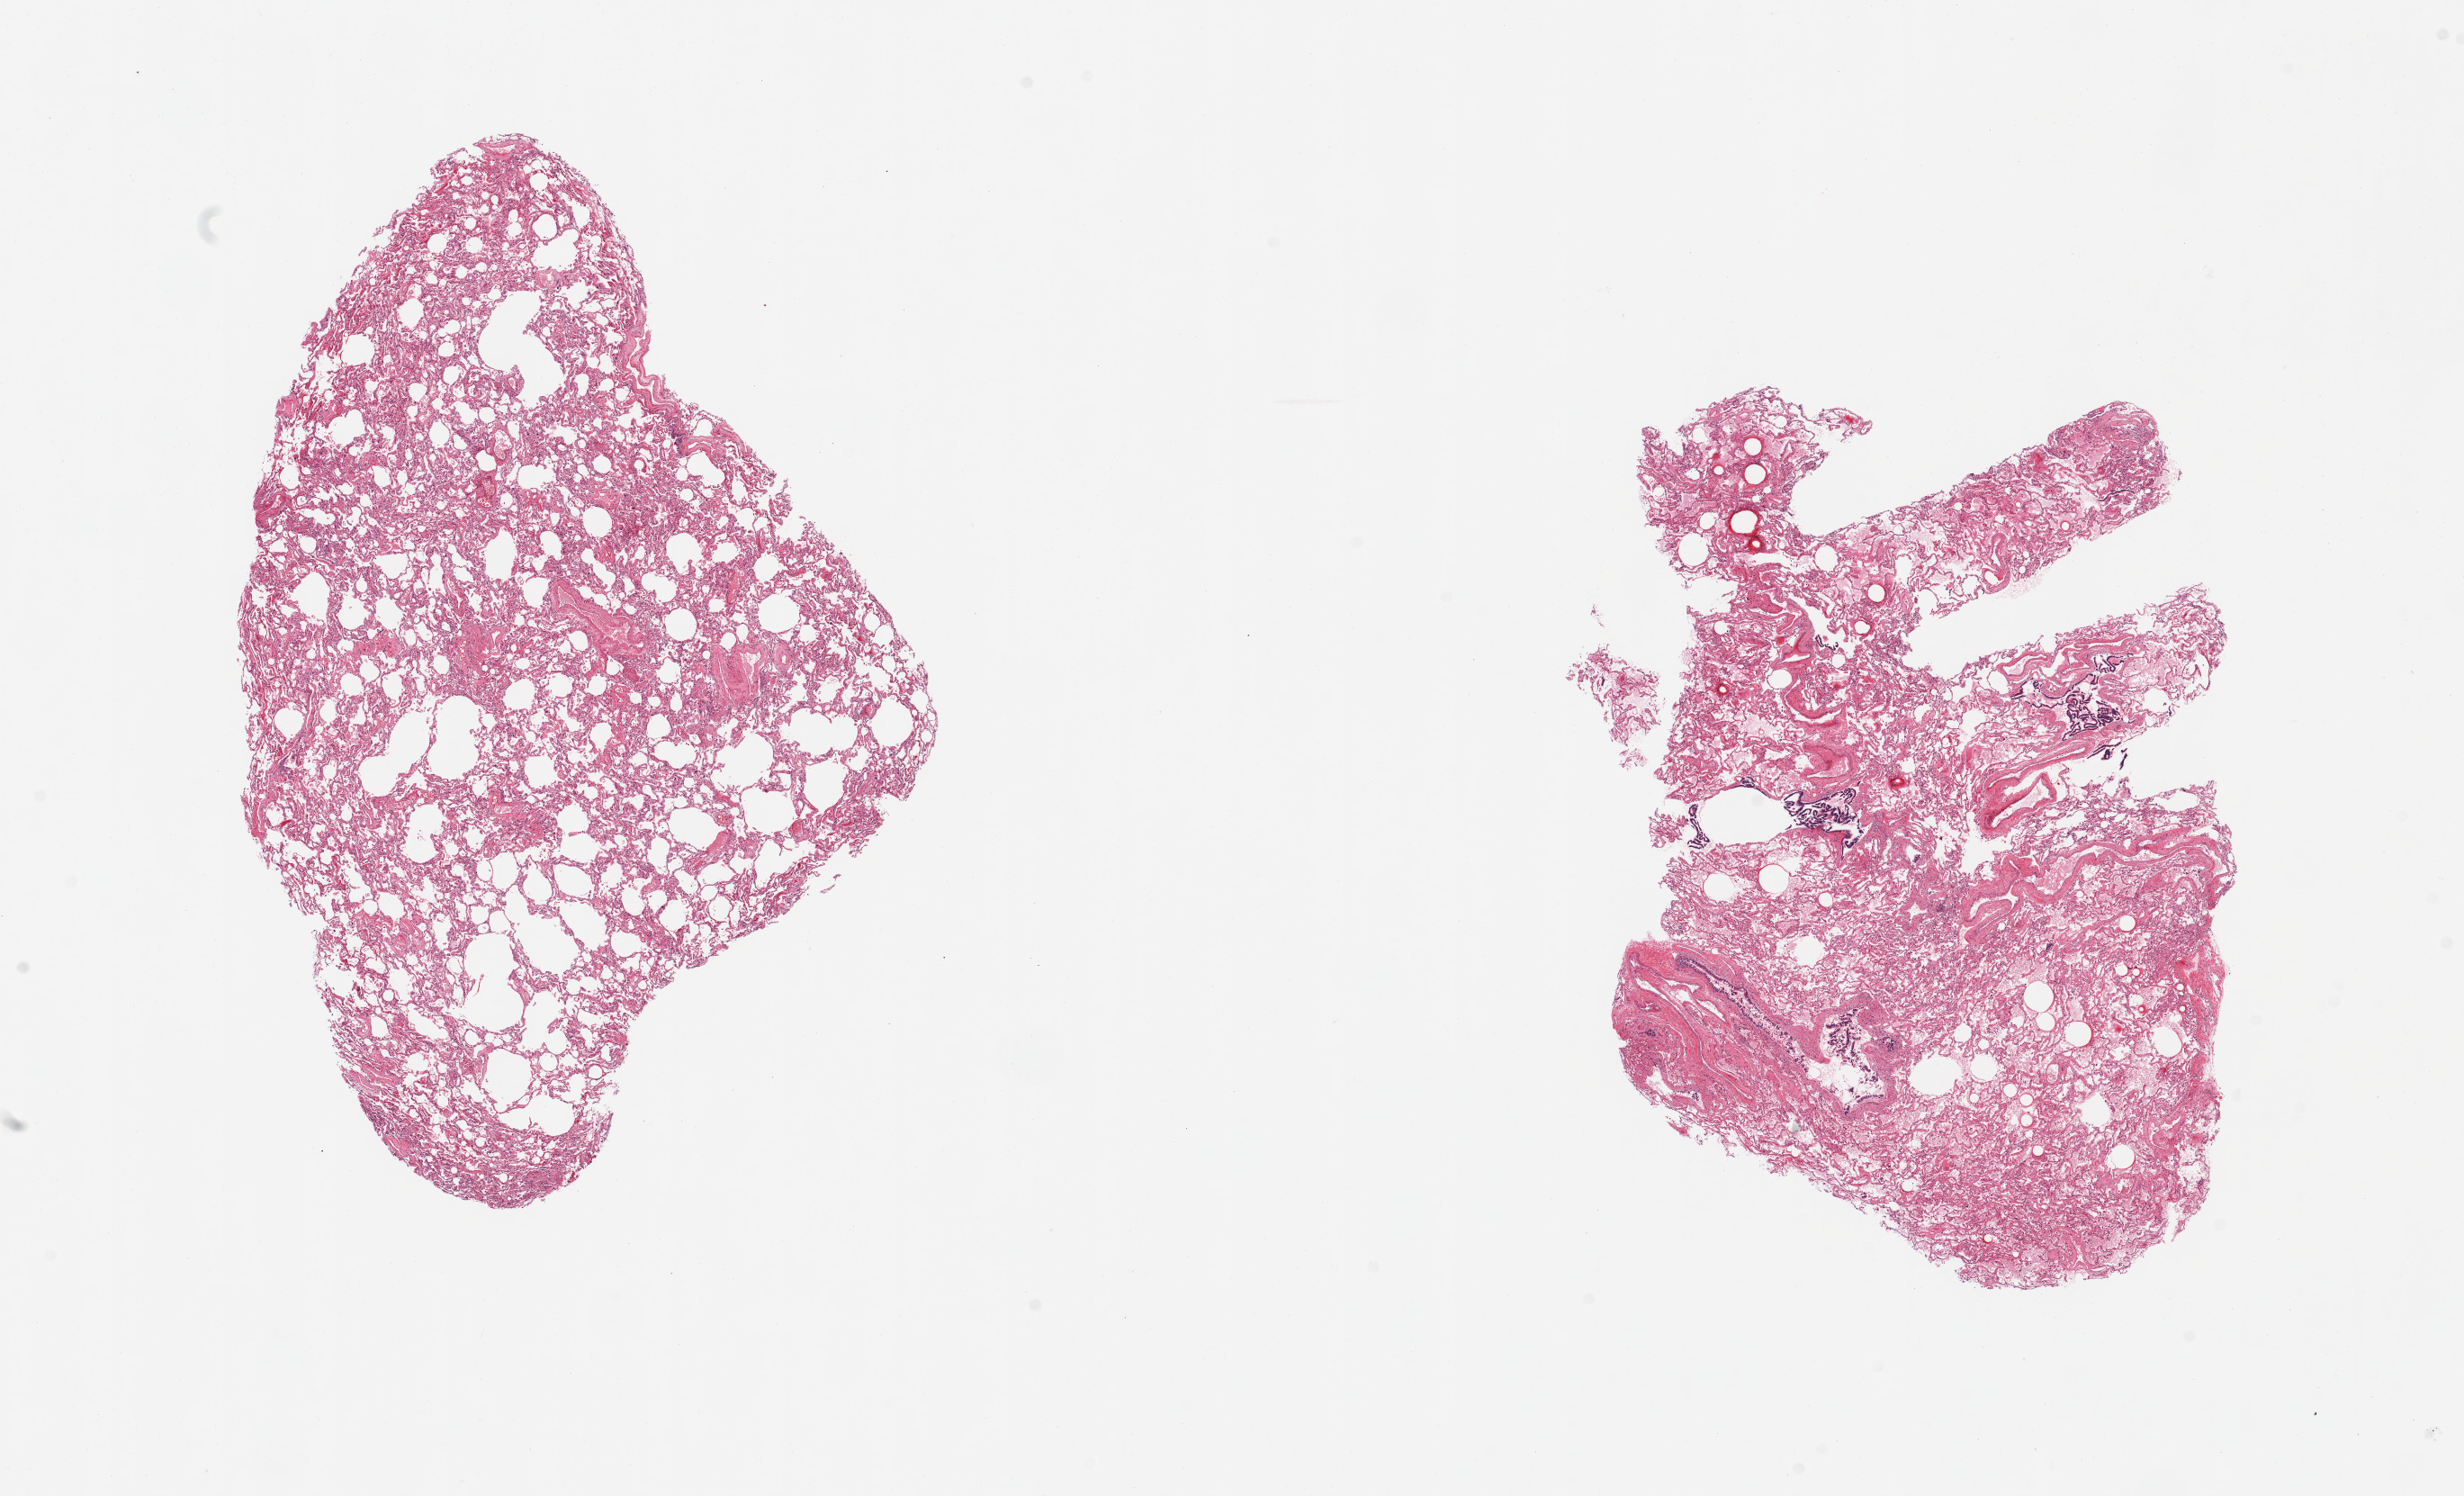
Whole-slide image, hematoxylin and eosin (H&E) stain — shown as a low-resolution overview of the whole scanned area (about 21.7 x 13.1 mm, slide scanned at 20x); PAXgene-fixed paraffin-embedded (PFPE) section; target tissue: lung; donor tissue sample. Donor sex: female.
Pathologist's review note for this sample: 2 pieces, mild congestion, partially sloughing bronchial mucosa.